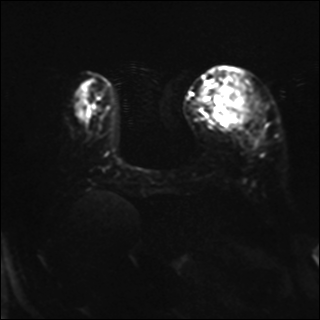
Breast MRI, one axial slice. Diffusion-weighted series; image 2 of 4 stored at this slice position (different b-values; order by instance number). 1.5 T. 320 × 320 image matrix, field of view 320 × 320 mm. Female patient.
Structures marked on this image (outlined manually by an expert reader):
- tumour on diffusion-weighted imaging: box from (x=218, y=82) to (x=256, y=114) px